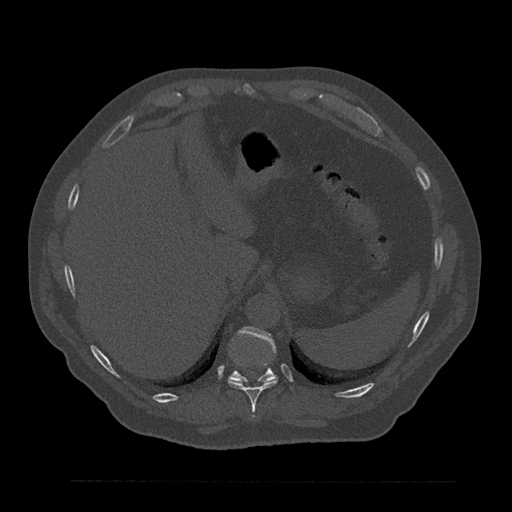
CT including the spine, one axial slice; position 327 of 797 along the scan axis; 120 kVp; bone window (W 1800 / L 400 HU); 0.5 mm slice thickness; 512 × 512 image matrix, field of view 430 × 430 mm. Male patient, age 61 years. Case-level facts recorded for this patient, not image findings: primary cancer: prostate.
Structures marked on this image (semi-automatic segmentation, software-assisted and operator-edited):
- T10 vertebra: bounding box [x1, y1, x2, y2] px = [228, 378, 278, 412]
- T11 vertebra: [229, 327, 277, 382]